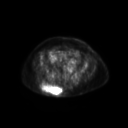
FDG PET of an extremity soft-tissue mass (from a PET/CT study), one axial slice. Position 72 of 267 along the scan axis. 3.27 mm slice thickness. 128 × 128 image matrix, field of view 600 × 600 mm. Patient: female, 60 years. Case-level facts recorded for this patient, not image findings: histological type: spindle cell suggestive of myxofibrosarcoma; grade: intermediate; site of the primary tumour: right buttock.
Outlined on this slice (expert contour drawn on MRI and transferred to this co-registered scan by the dataset authors):
- gross tumour volume (mass): bounding box (x1, y1, x2, y2) in pixels: (39, 83, 63, 96)